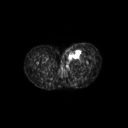
FDG PET of an extremity soft-tissue mass (from a PET/CT study), one axial slice. Slice 45 of 267 in the series (ordered by position). 3.27 mm slice thickness. 128 × 128 image matrix. Patient: female, 24 years. Case-level facts recorded for this patient, not image findings: histological type: leiomyosarcoma; grade: high; site of the primary tumour: groin.
Structures marked on this image (expert contour drawn on MRI and transferred to this co-registered scan by the dataset authors):
- gross tumour volume including surrounding oedema: box from (x=61, y=47) to (x=81, y=64) px
- gross tumour volume (mass): (x=69, y=49)–(x=80, y=57)